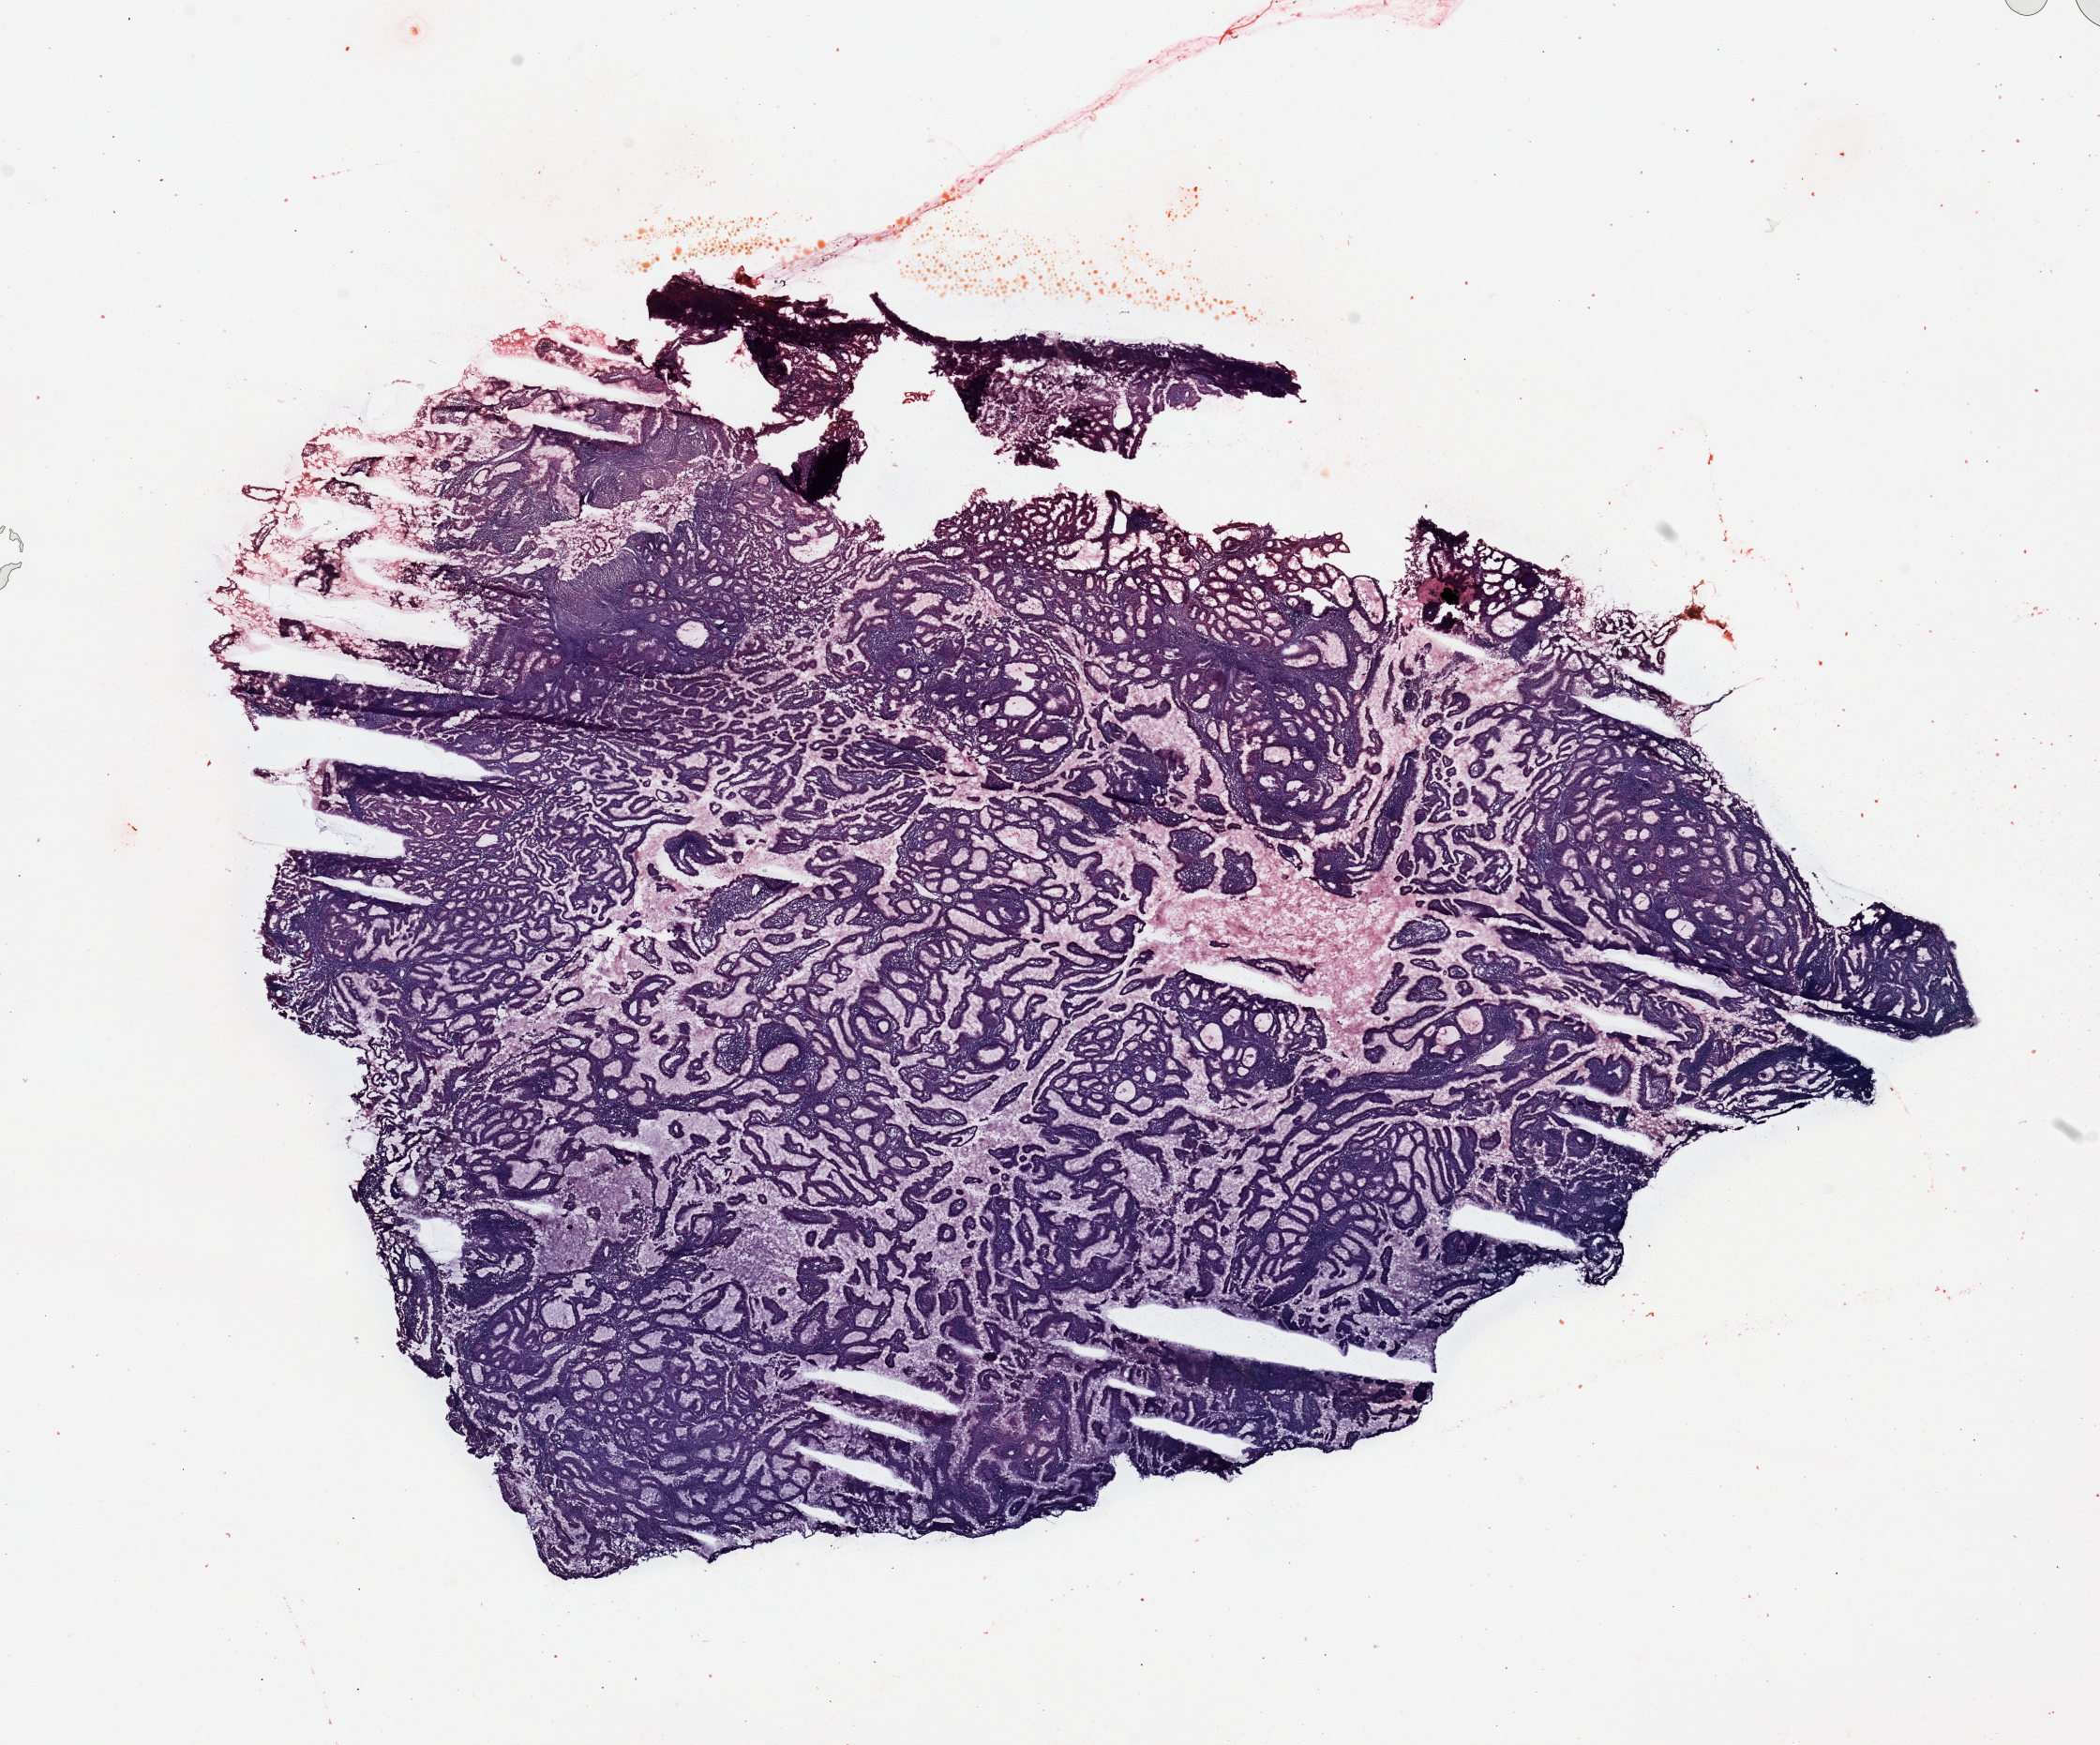
Digitized H&E tissue section (whole slide) — a low-resolution overview of the entire scanned area, about 17.7 x 14.7 mm; tumour tissue sample, uterus. Patient: female, age 61 years. Histologic grade: G1 (well differentiated).
AJCC pathologic stage: I. Histologic diagnosis: Endometrioid adenocarcinoma, NOS.